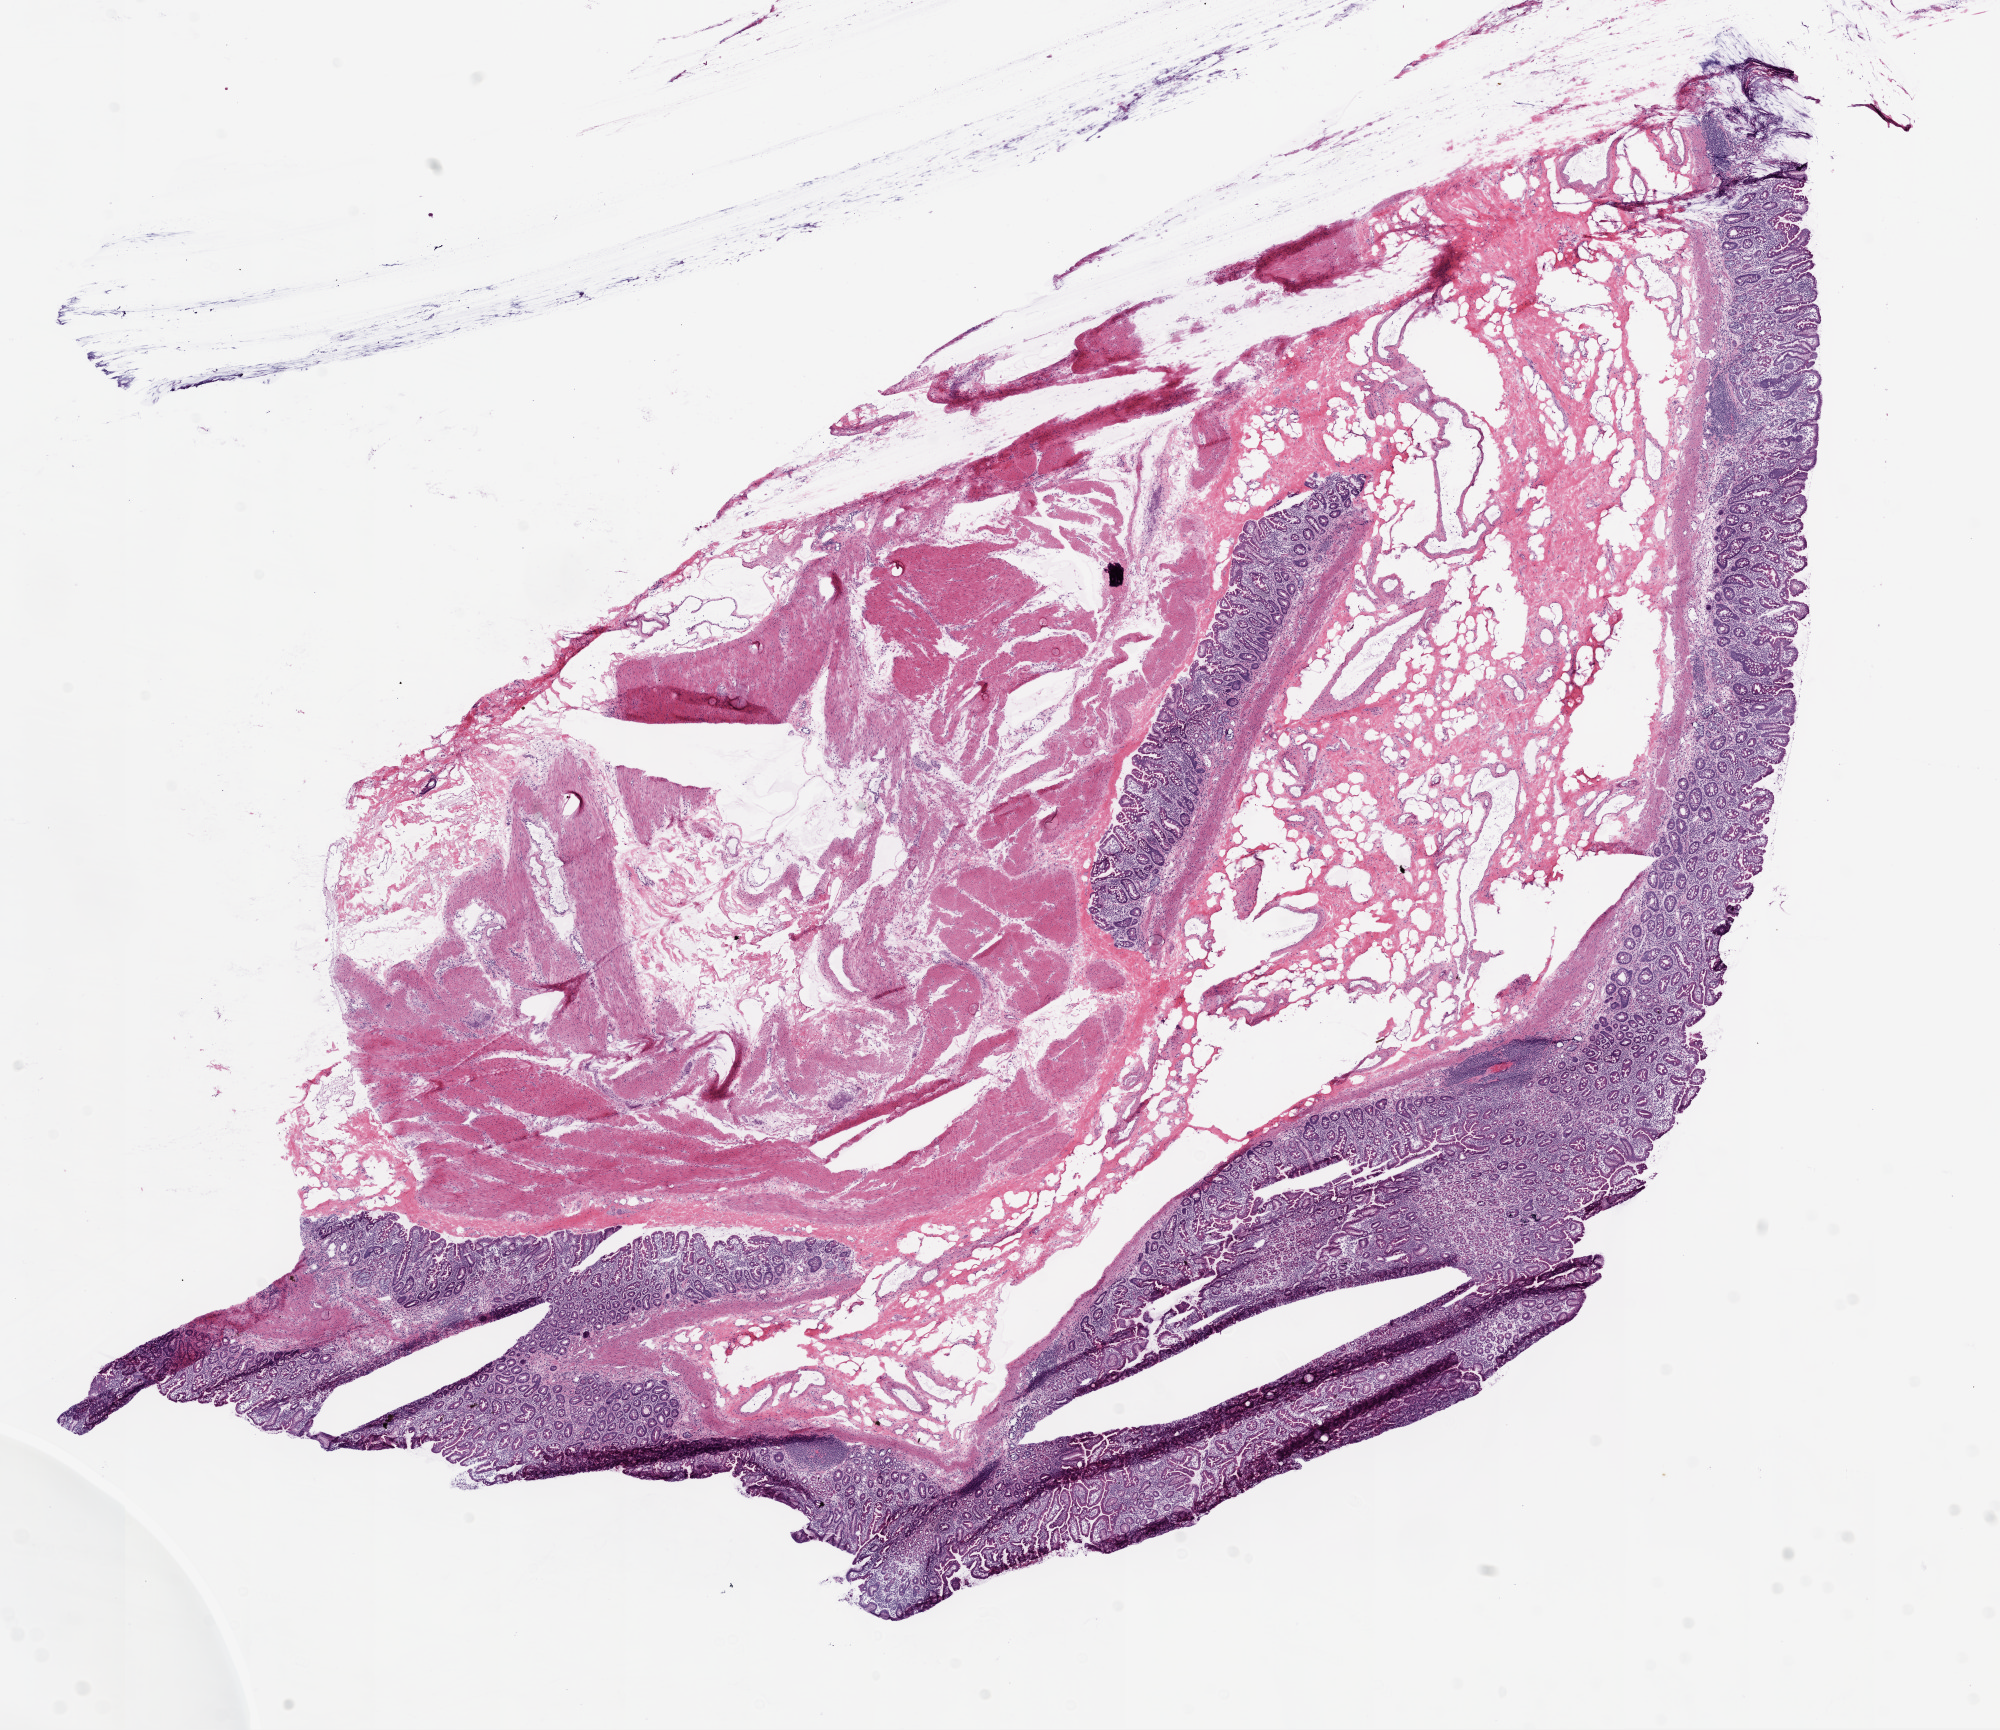
Whole-slide histology image, H&E — a low-resolution overview of the entire scanned area, about 16.0 x 13.9 mm, frozen section, stomach, solid tissue normal (non-tumour tissue) sample. Patient: female, age at initial diagnosis 71 years.
This section: solid tissue normal sample (biorepository sample class). Patient diagnosis: Adenocarcinoma, NOS (body of stomach).